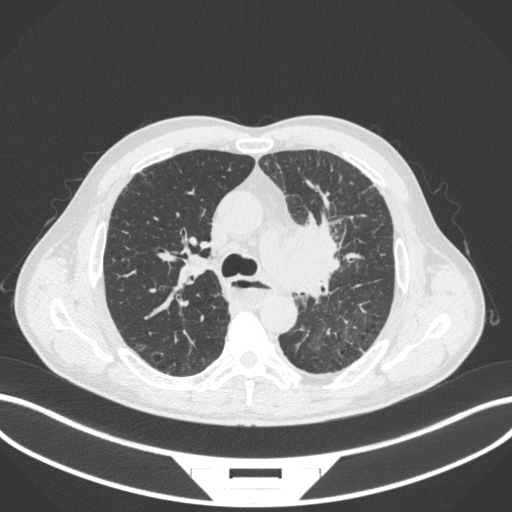
Chest CT, one axial slice. Position 254 of 411 along the scan axis. Lung window (W 1500 / L -600 HU). 1 mm slice thickness. 512 × 512 image matrix, field of view 400 × 400 mm. Male patient, age 57 years. From the clinical record (not read from this slice): clinical TNM (as recorded): T2a N1 M0.
Structures marked on this image (bounding box drawn by a radiologist):
- lung tumour (recorded histology: squamous cell carcinoma): bounding box [x1, y1, x2, y2] px = [257, 211, 348, 307]